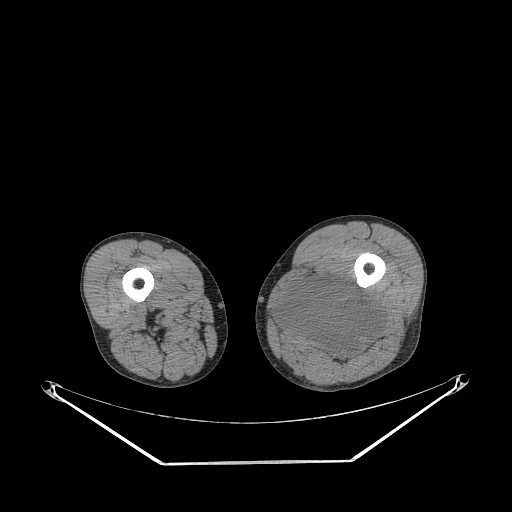
CT of an extremity soft-tissue mass (from a PET/CT study), one axial slice; slice 229 of 267 in the series (ordered by position); 140 kVp; soft-tissue window (W 400 / L 40 HU); 3.75 mm slice thickness; 512 × 512 image matrix, field of view 500 × 500 mm. Male patient. From the clinical record (not read from this slice): histological type: undifferentiated pleomorphic liposarcoma; grade: high; site of the primary tumour: left thigh.
Annotated regions visible in this slice (expert contour drawn on MRI and transferred to this co-registered scan by the dataset authors):
- gross tumour volume including surrounding oedema: box from (x=274, y=276) to (x=382, y=362) px
- gross tumour volume (mass): (x=276, y=276)–(x=382, y=362)